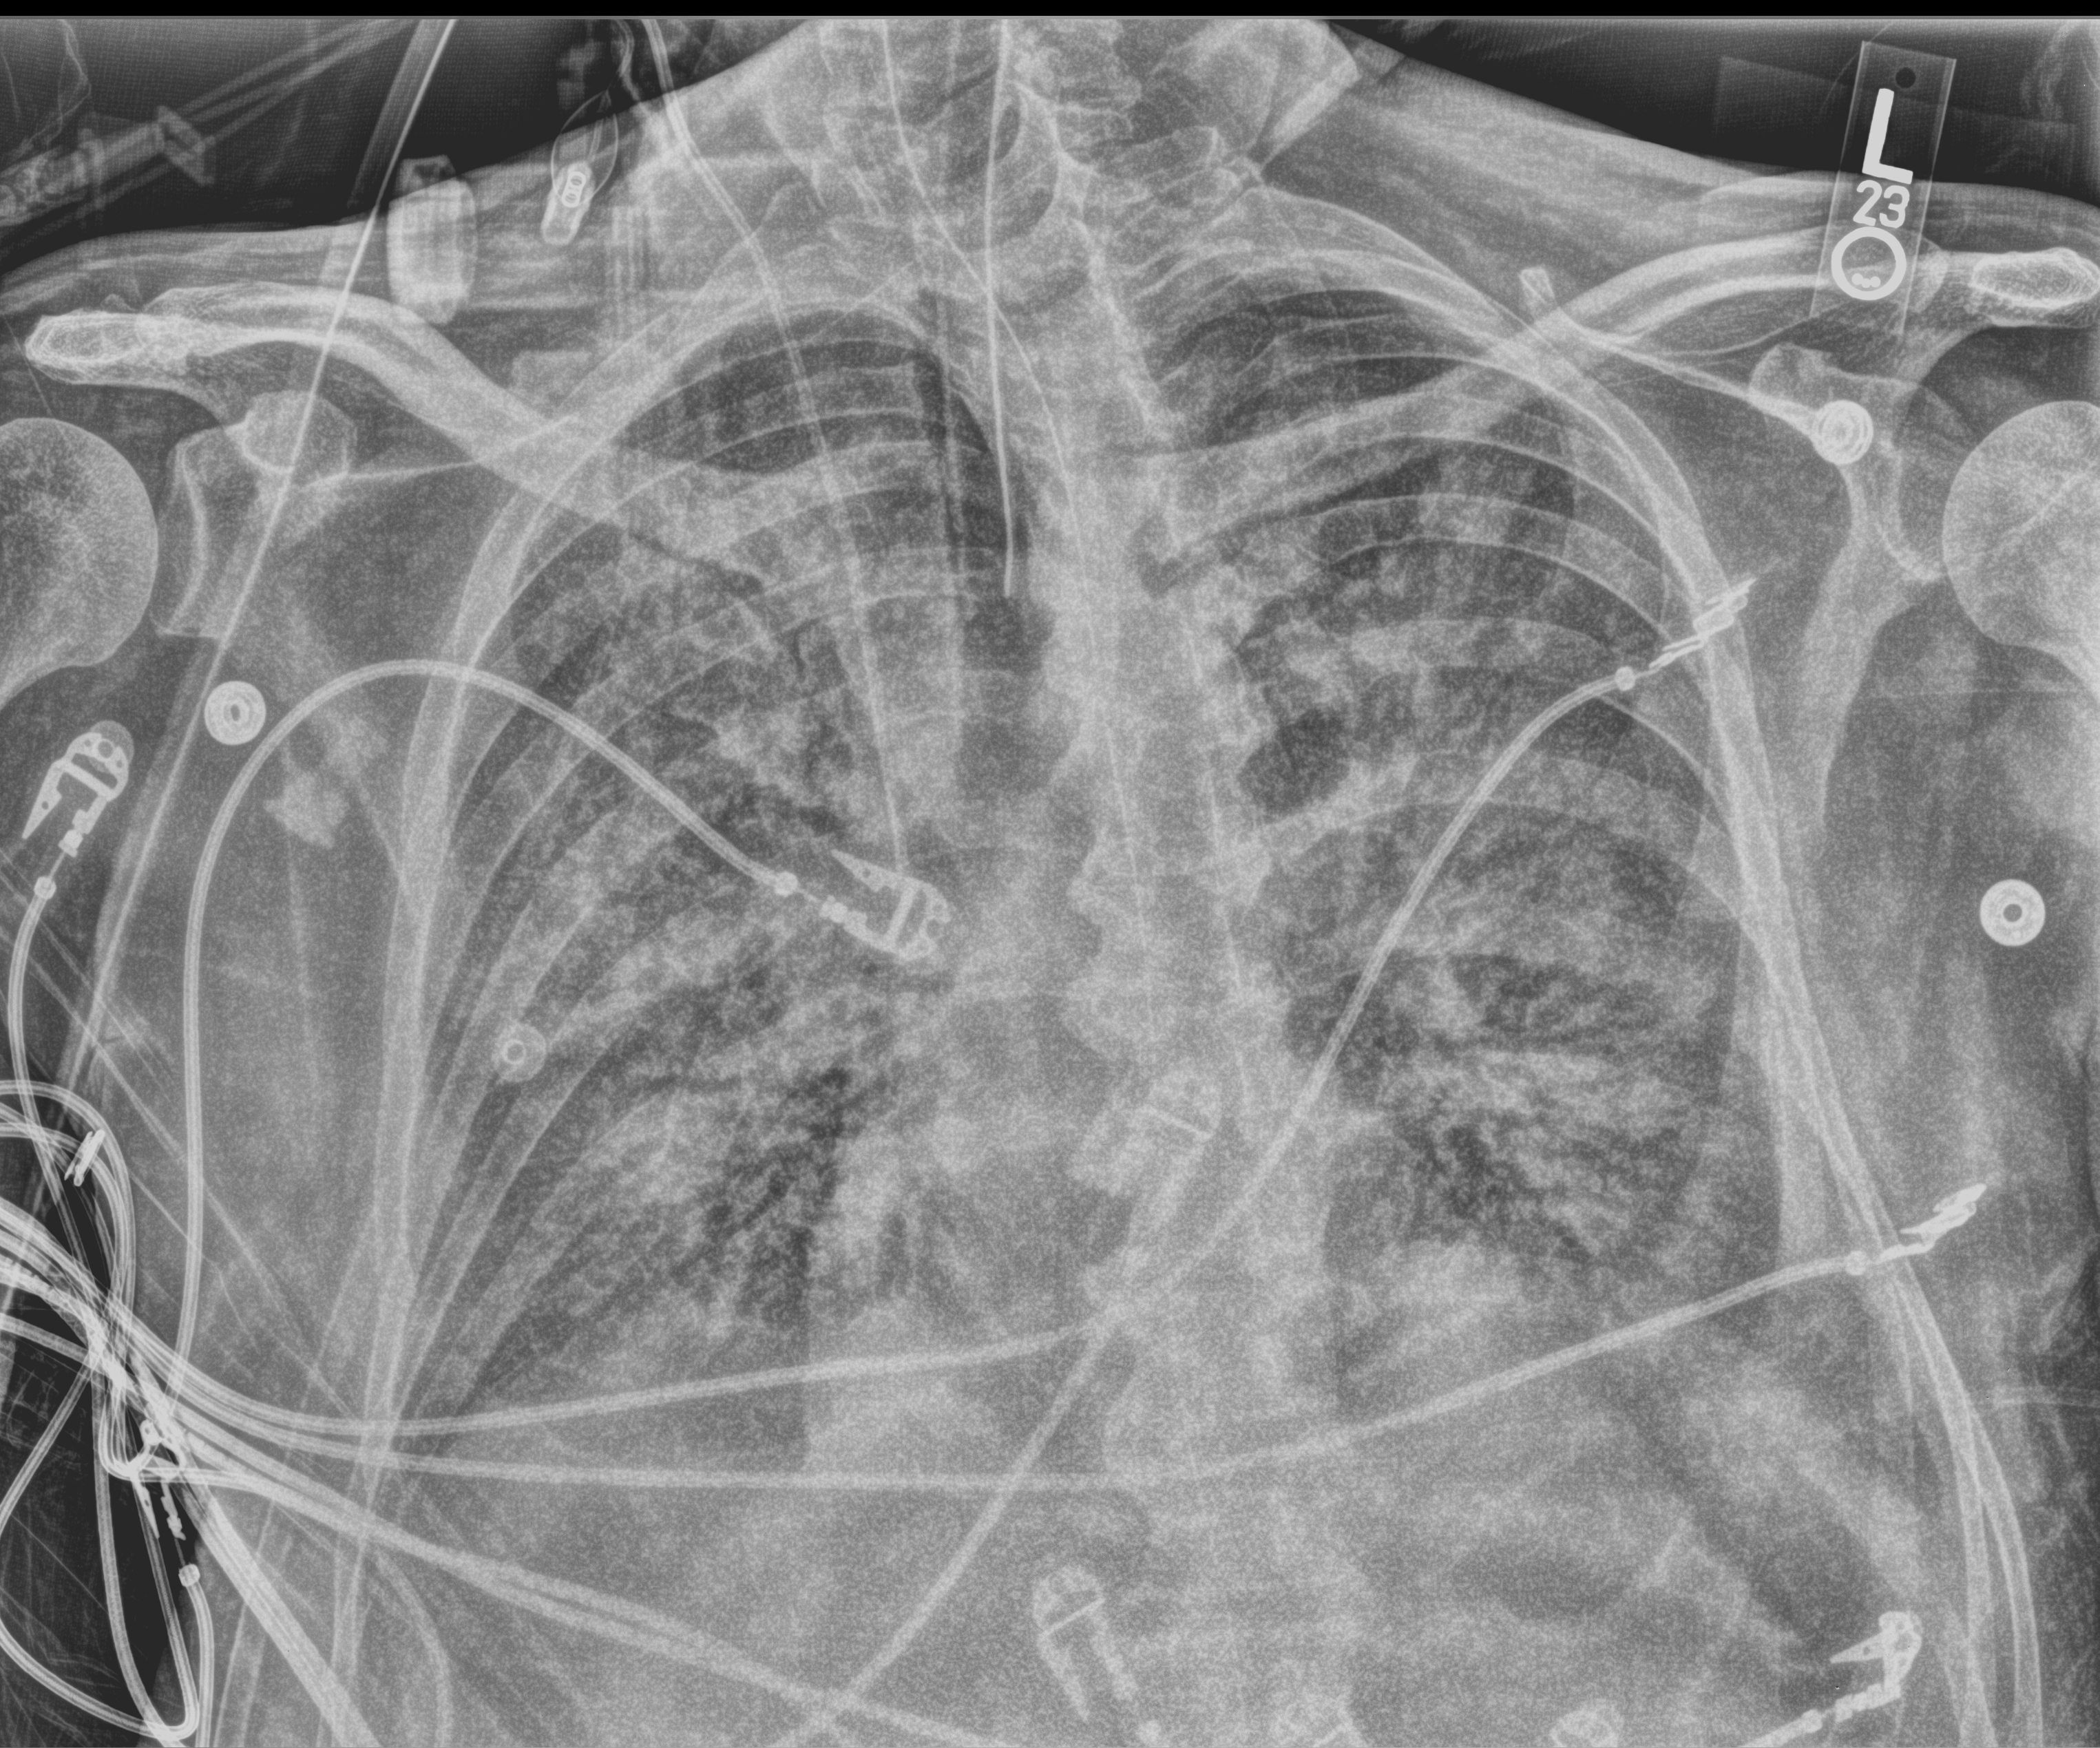
Portable chest radiograph; anteroposterior (AP) projection. Male patient hospitalised with COVID-19, age 60–74 years.
Admission-level facts for this patient (not findings on this image; timing relative to this image not recorded): mechanically ventilated during this hospital stay: yes; other chronic lung disease (admission record): no.